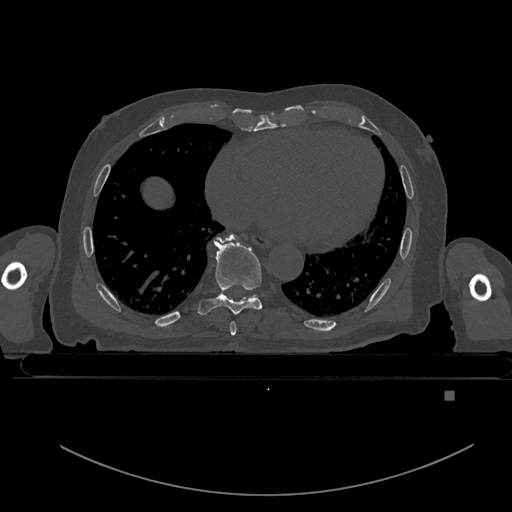
CT including the spine, one axial slice; position 199 of 969 along the scan axis; bone window (W 1800 / L 400 HU); 0.5 mm slice thickness; 512 × 512 image matrix, field of view 456 × 456 mm. Male patient, age 82 years. From the clinical record (not read from this slice): primary cancer: prostate; vertebrae with lytic lesions (as recorded): T11, T9, T8, T2.
Outlined on this slice (semi-automatically segmented with operator editing):
- T7 vertebra: bounding box (x1, y1, x2, y2) in pixels: (230, 321, 236, 335)
- T8 vertebra: (198, 236, 271, 318)
- T9 vertebra: (217, 235, 234, 297)